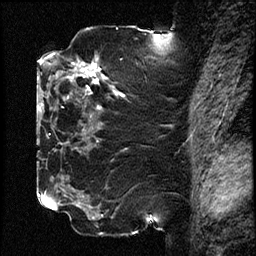
Breast MRI (dynamic contrast-enhanced), one sagittal slice. Slice 46 of 78 in the series (ordered by position). Dynamic contrast-enhanced study with each time point stored as its own series, time point 2 of 3 at this slice position (early post-contrast, ordered by acquisition time). 1.5 T. TE 4.2 ms, TR 17.6 ms. 2 mm slice thickness. 256 × 256 image matrix. Female patient, age 42 years. Case-level facts recorded for this patient, not image findings: setting: breast cancer imaged before/during neoadjuvant chemotherapy; receptor status: HER2-positive.
Annotated regions visible in this slice (semi-automatically segmented with operator editing):
- analysis volume of interest (the breast-tissue region the enhancement analysis was run in; not a lesion): bounding box (x1, y1, x2, y2) in pixels: (50, 48, 130, 129)
- tumour enhancement mask (voxels above the 100 % enhancement threshold inside the analysis volume of interest): (70, 62, 123, 96)